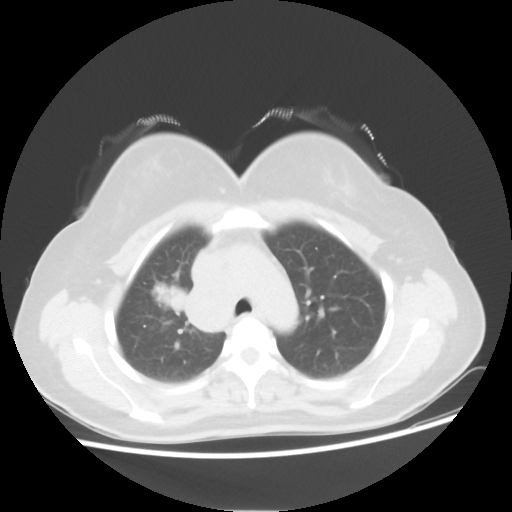
Chest CT, one axial slice. Slice 37 of 50 in the series (ordered by position). Reconstruction kernel STANDARD. Lung window (W 1500 / L -600 HU). 512 × 512 image matrix, field of view 360 × 360 mm. Patient: female, 40 years. Case-level facts recorded for this patient, not image findings: clinical TNM (as recorded): T1c N3 M0; histopathological grade: G3.
Outlined on this slice (rectangle marked by the reading radiologist):
- lung tumour (recorded histology: small cell carcinoma): bounding box <154,282,185,315> (left, top, right, bottom; pixels)